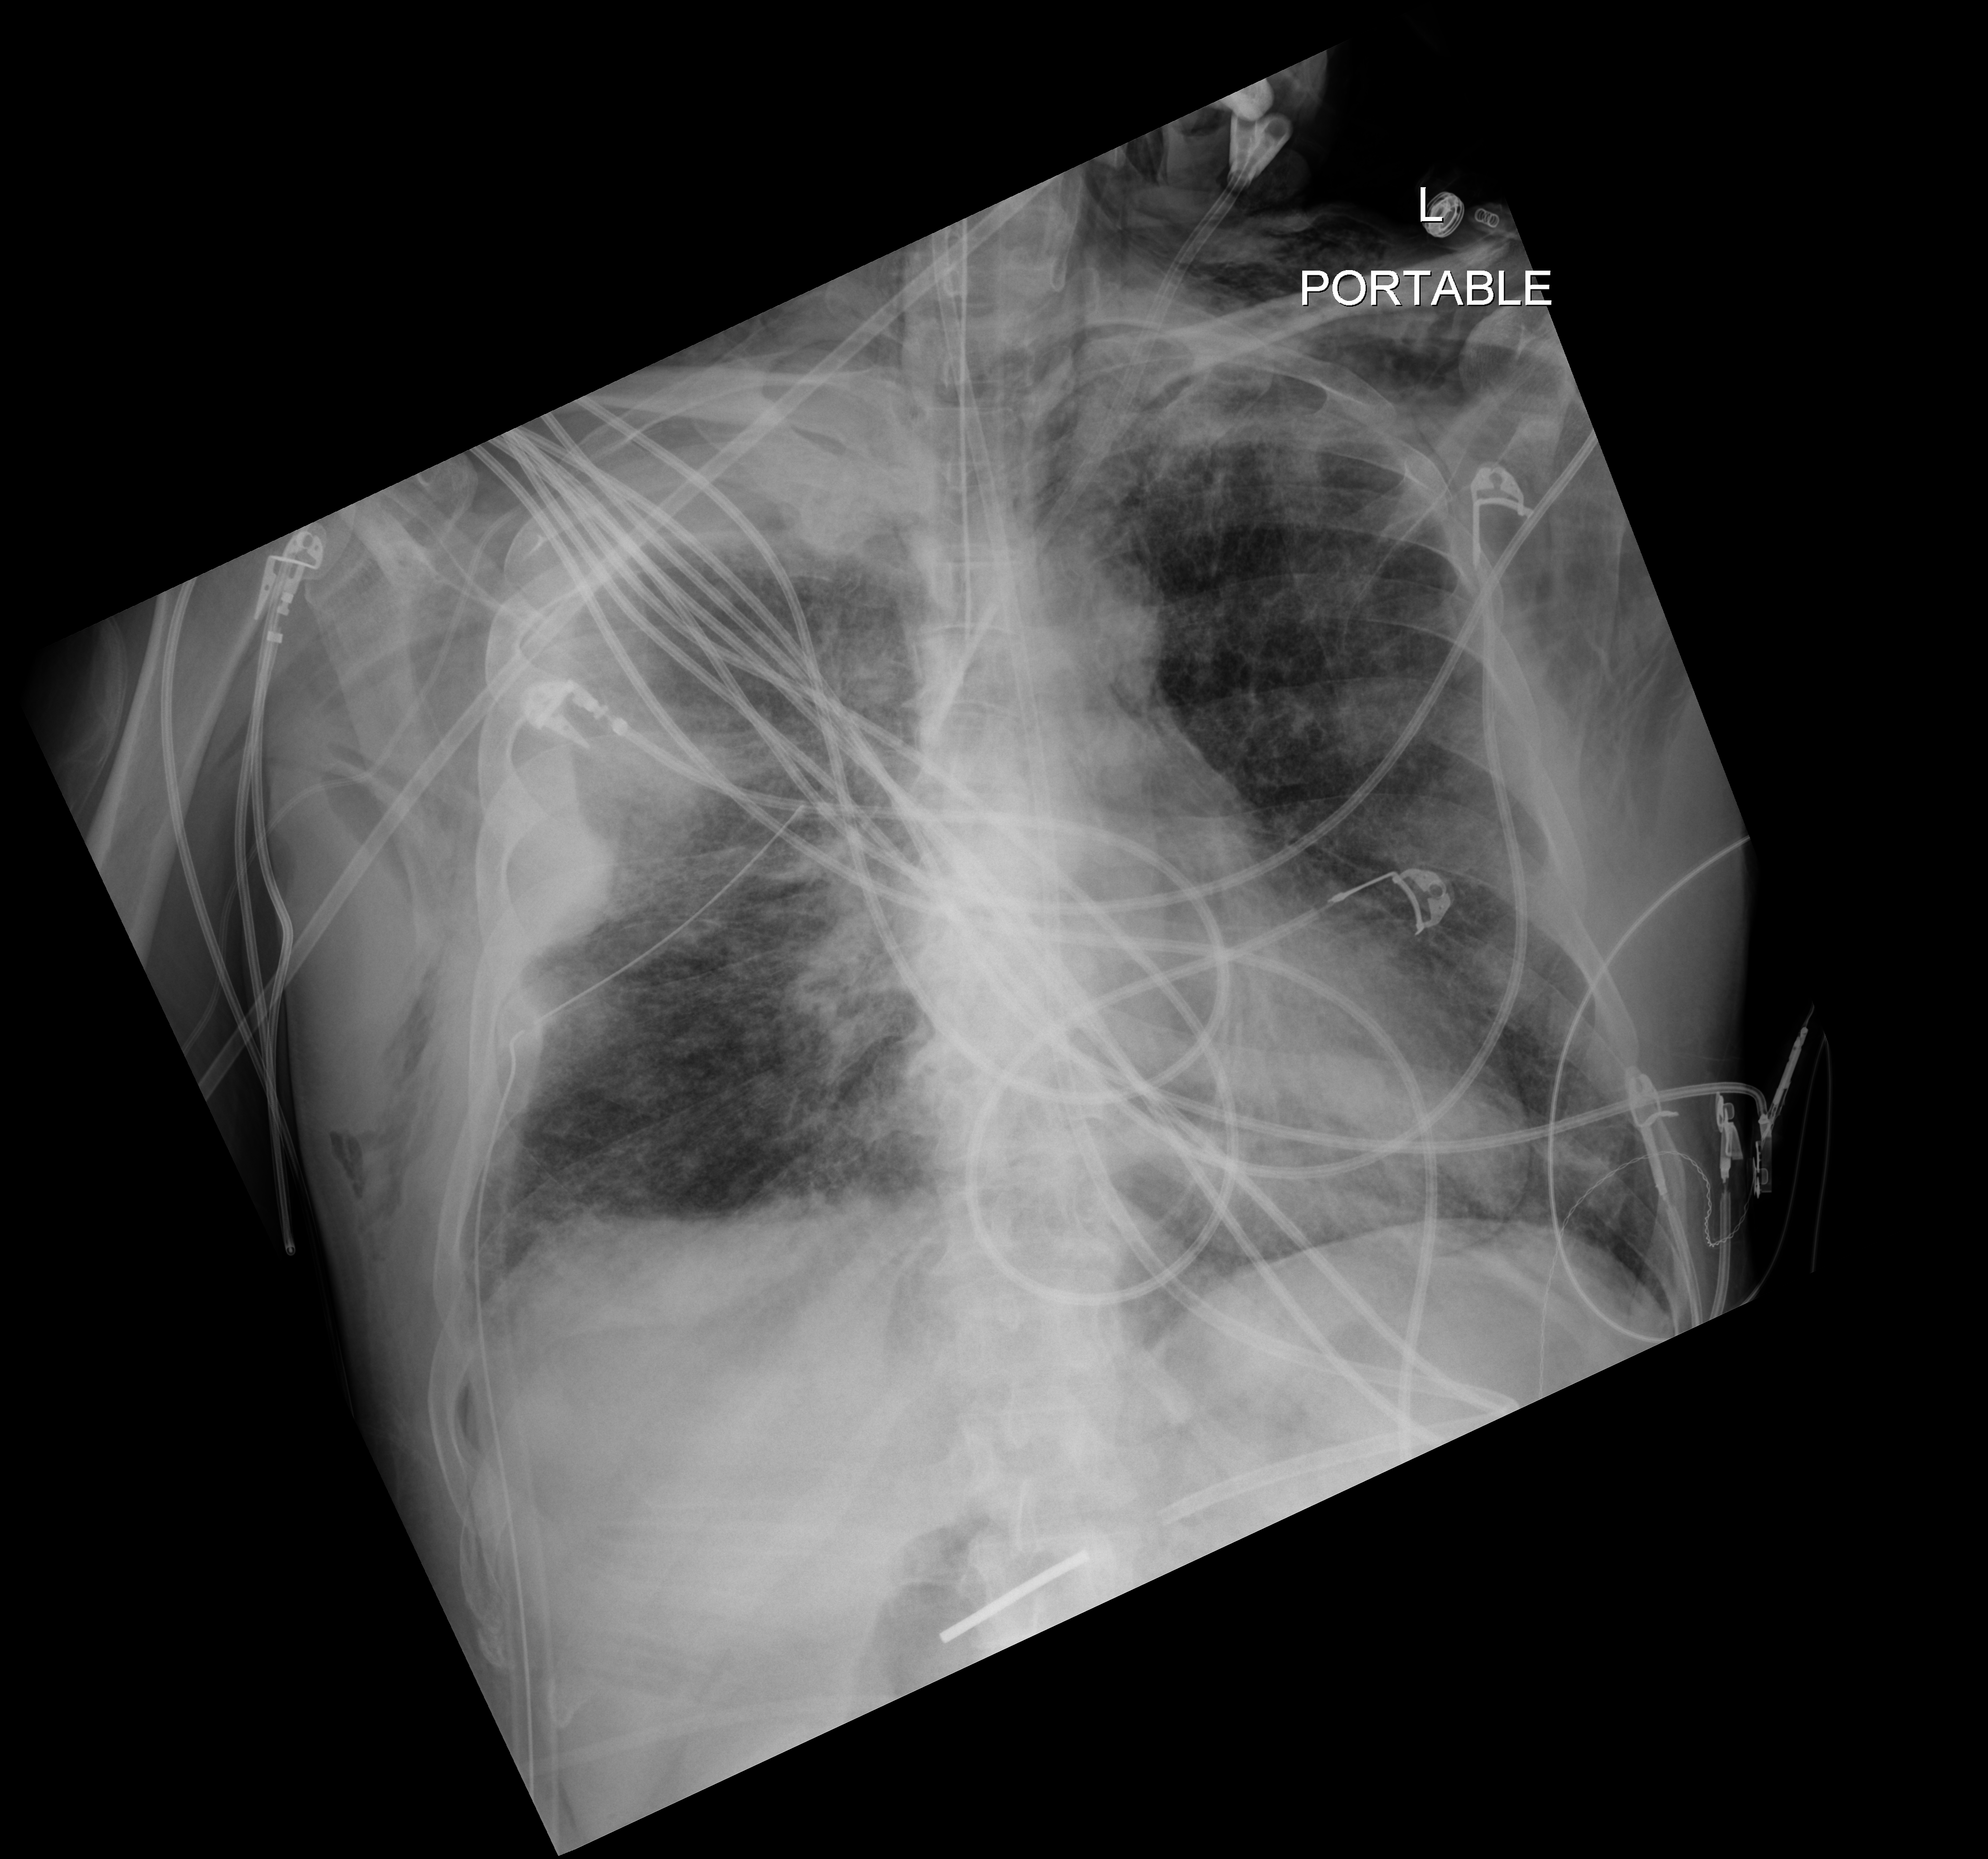
Bedside chest radiograph (digital radiography). Patient hospitalised with COVID-19; male, aged 18–59 years.
Admission-level facts for this patient (not findings on this image; timing relative to this image not recorded):
- admitted to intensive care during this hospital stay: yes